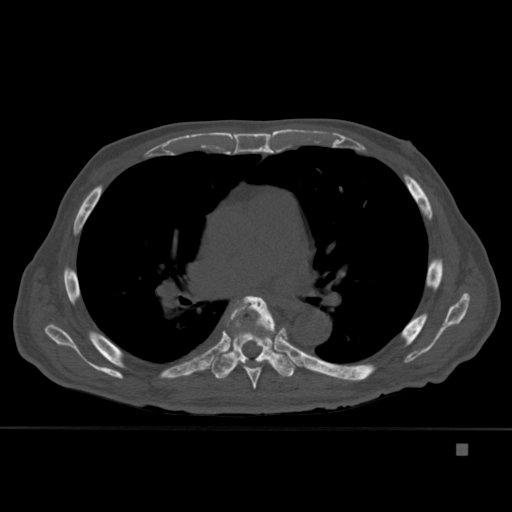
CT including the spine, one axial slice; slice 286 of 451 in the series (ordered by position); bone window (W 1800 / L 400 HU); 1.5 mm slice thickness; 512 × 512 image matrix, field of view 378 × 378 mm. Male patient, age 75 years. From the clinical record (not read from this slice): primary cancer: prostate.
Structures marked on this image (semi-automatic segmentation, software-assisted and operator-edited):
- T4 vertebra: bounding box [x1, y1, x2, y2] px = [270, 328, 286, 333]
- T6 vertebra: [230, 295, 277, 389]
- T7 vertebra: [210, 301, 296, 379]